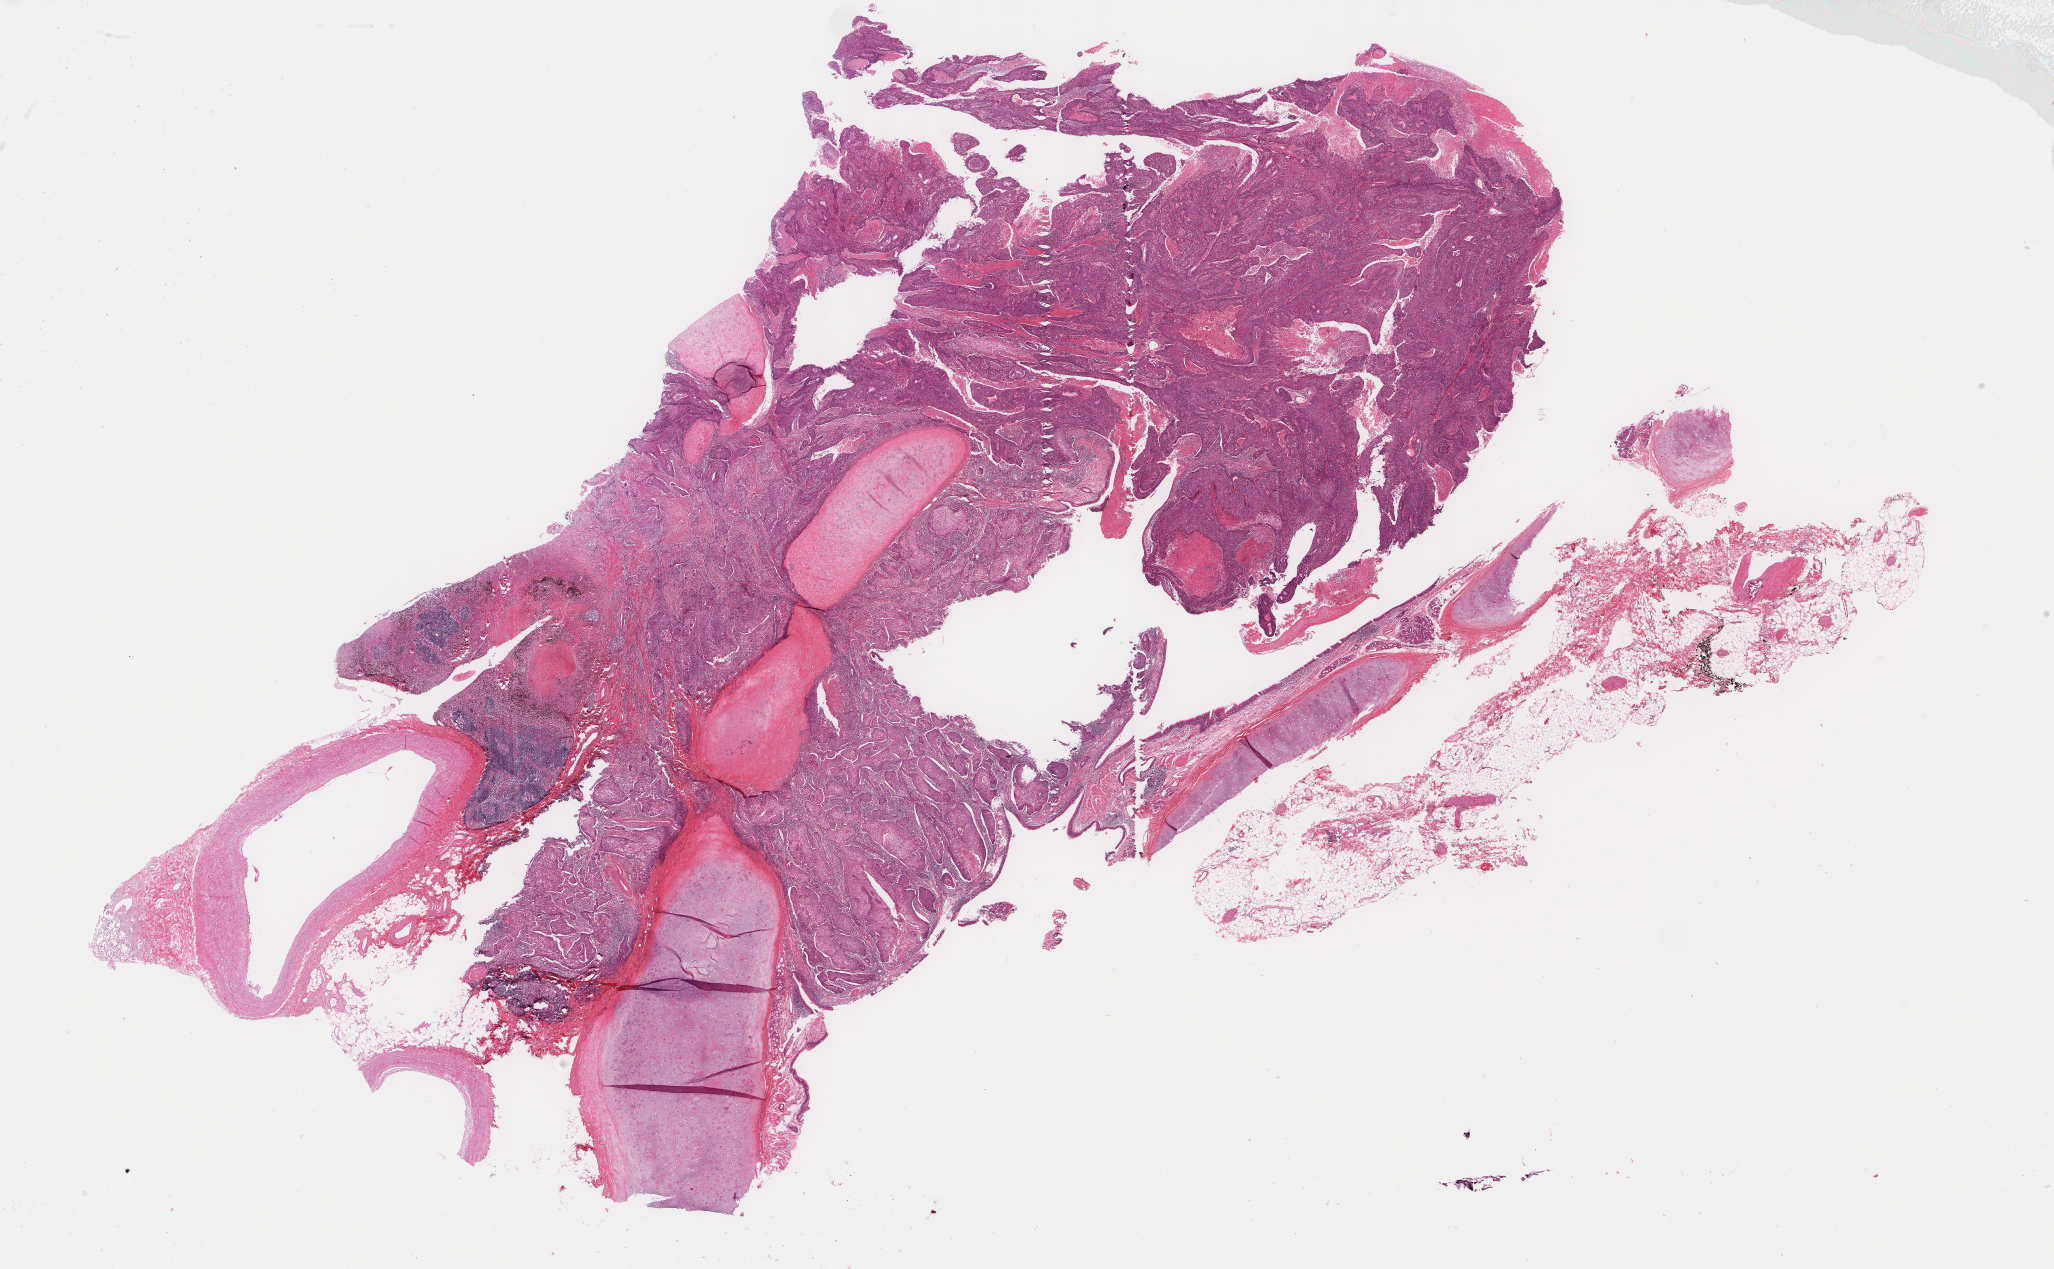
Digitized Hematoxylin and eosin (H&E) stained tissue section (whole slide) — shown as a low-resolution overview of the whole scanned area (about 33.2 x 20.5 mm, from a 40x scan), formalin-fixed paraffin-embedded (FFPE) diagnostic section, primary tumour sample from the lung. Female patient; age at initial diagnosis 62 years.
Diagnosis: Squamous cell carcinoma, keratinizing, NOS.